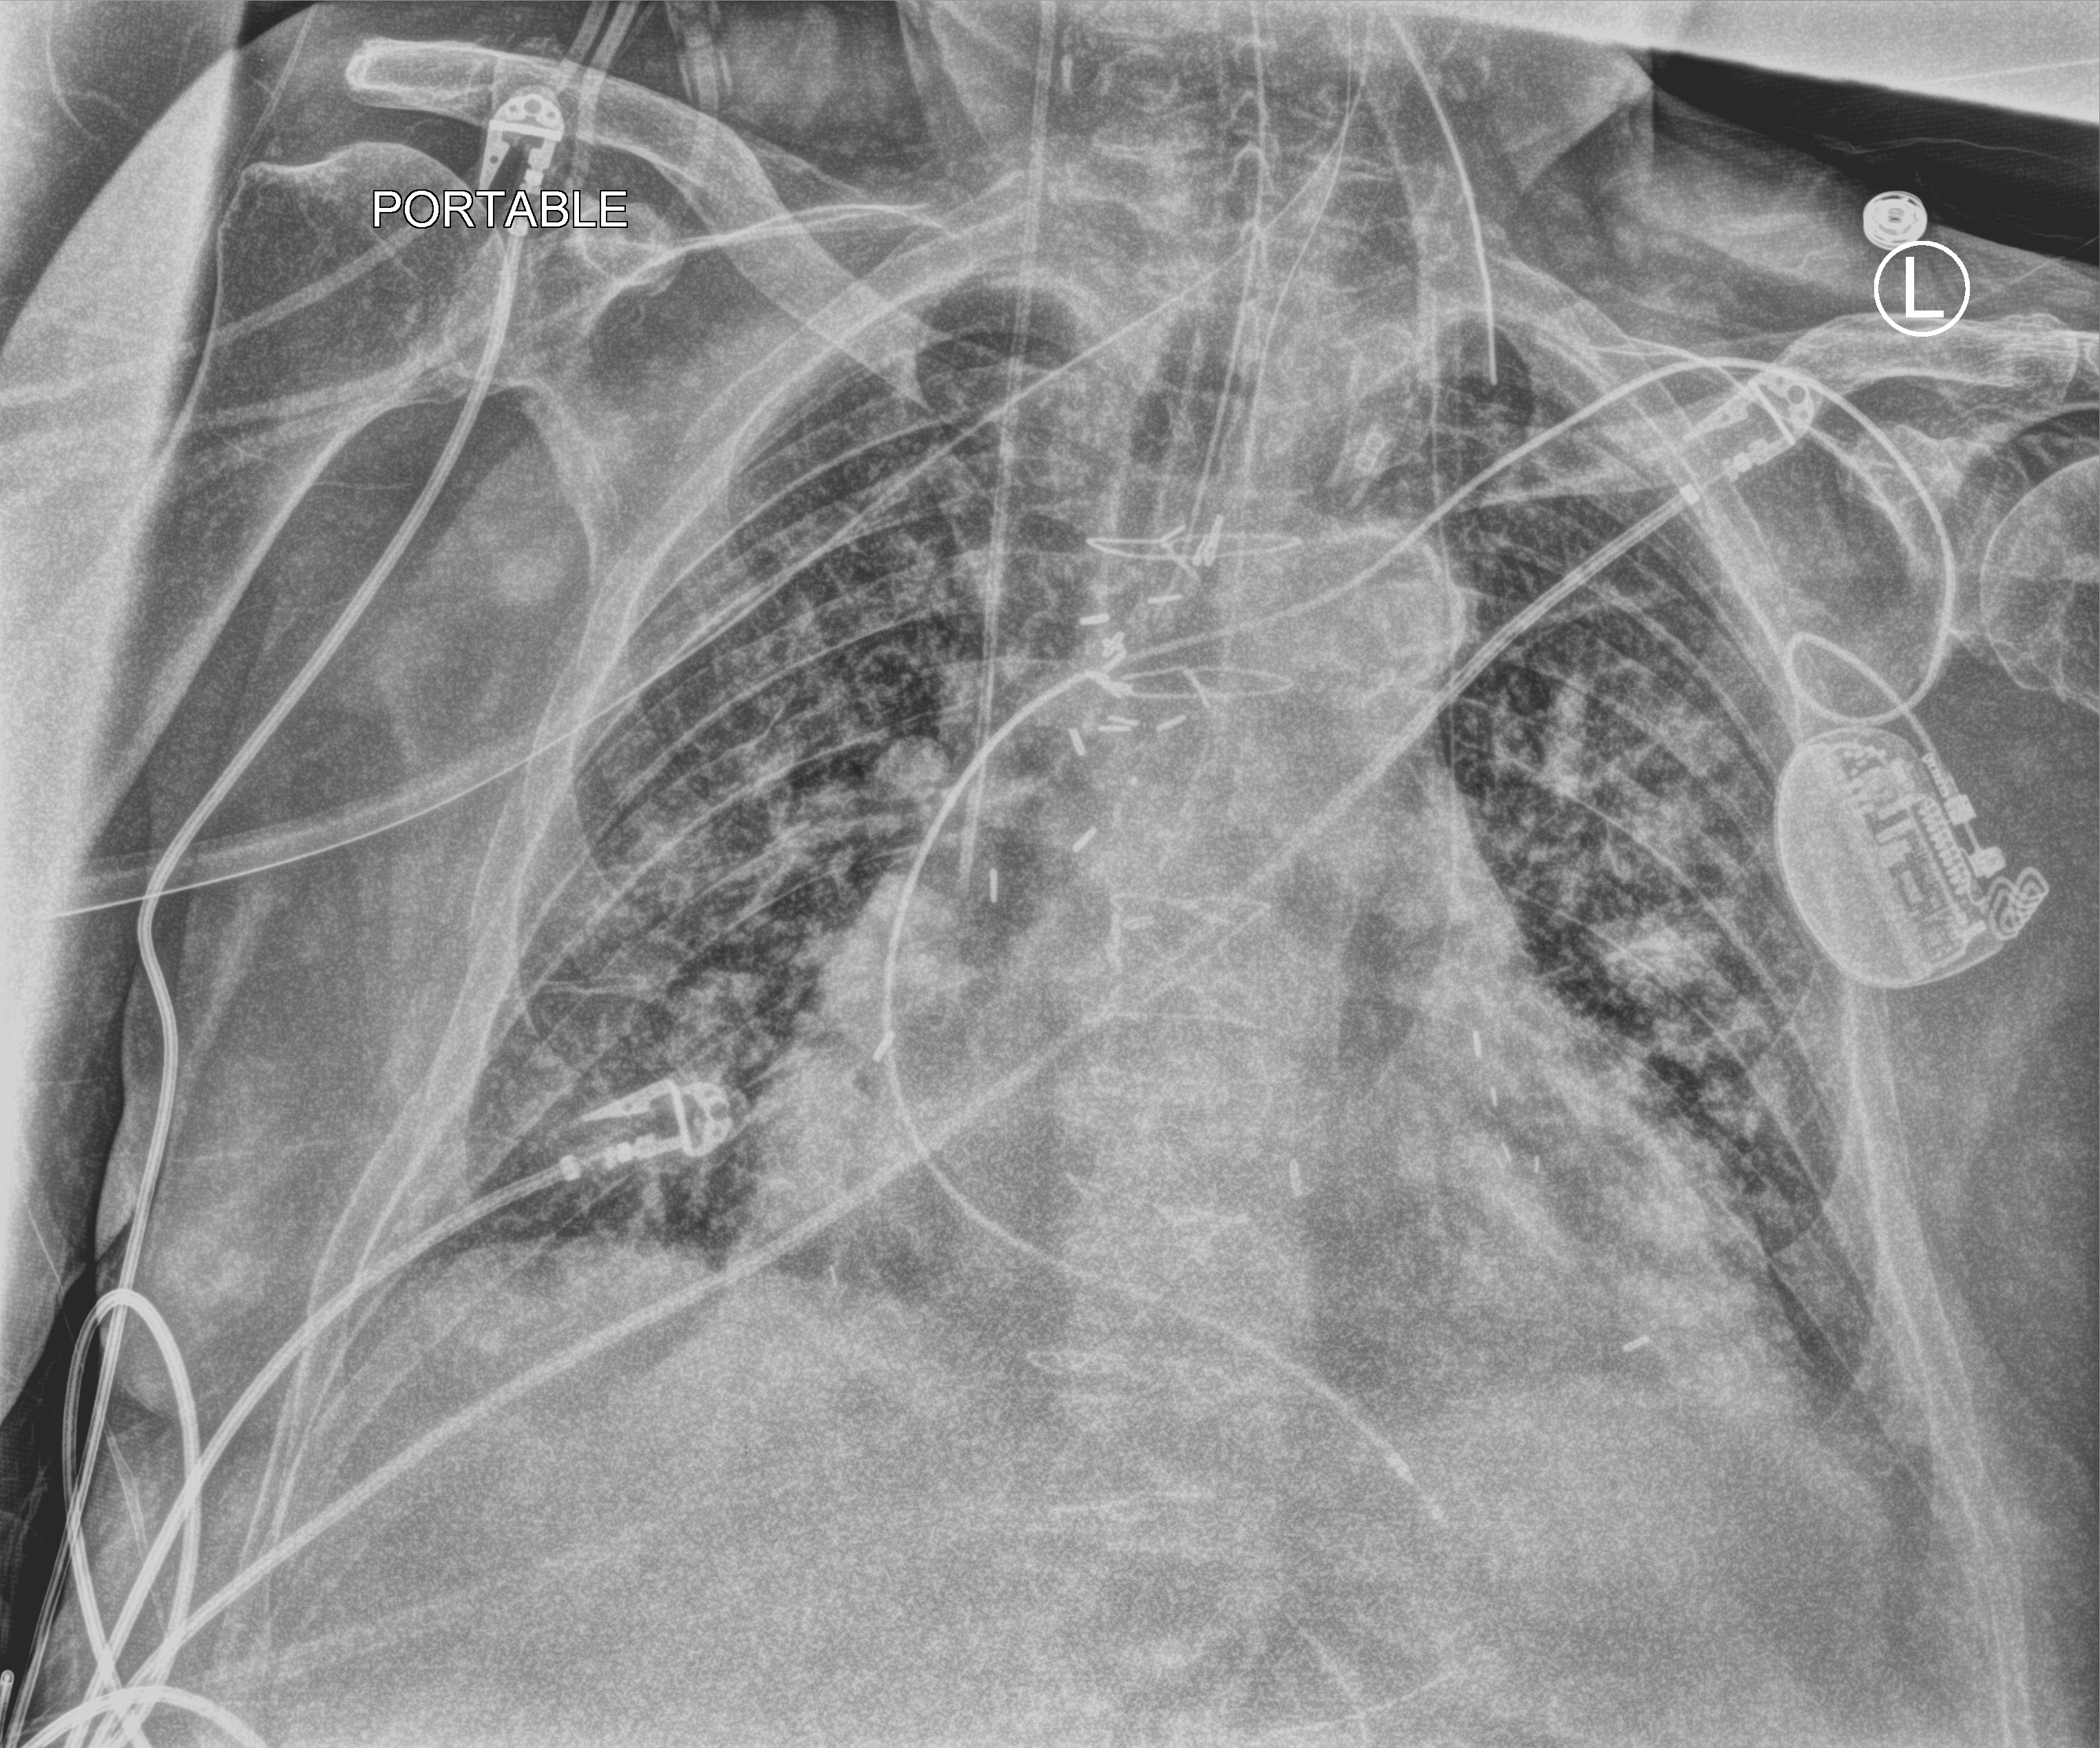
Bedside chest radiograph (computed radiography), anteroposterior (AP) projection. Male patient hospitalised with COVID-19, age 75–90 years.
Hospital-stay facts (about this admission, not read from this image; timing relative to this image not recorded):
- other chronic lung disease (admission record): yes